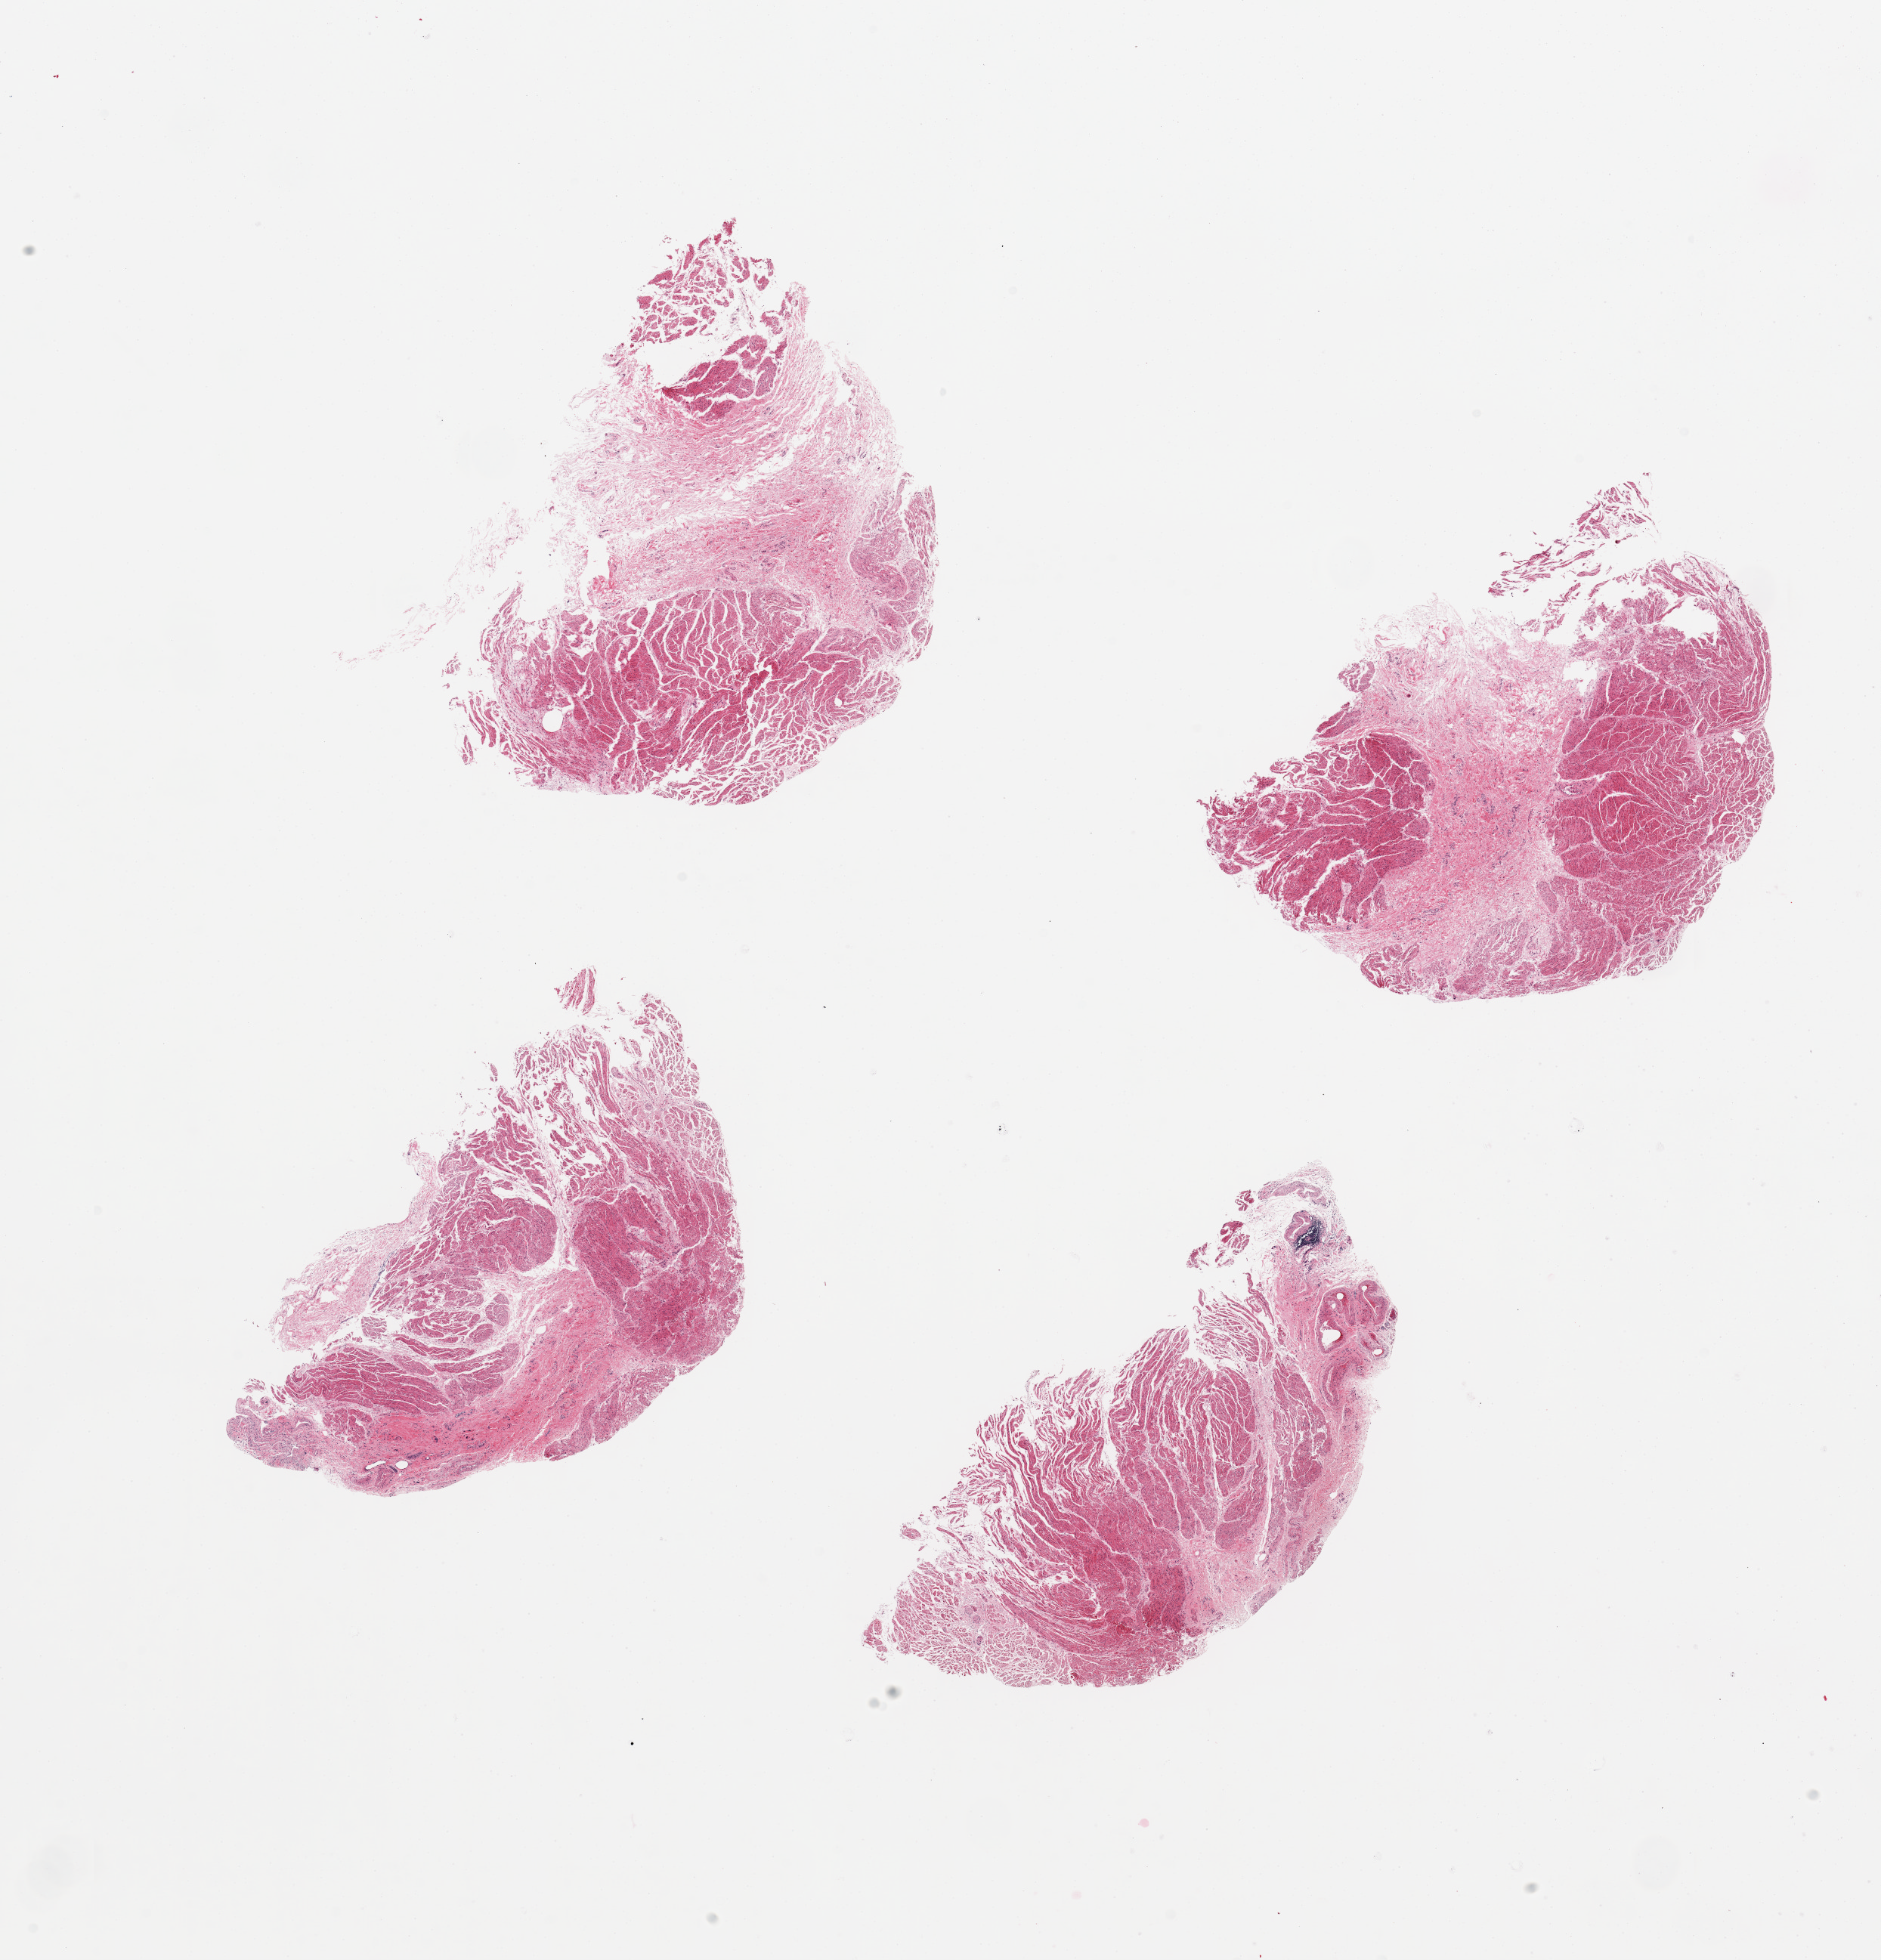
Whole-slide image, hematoxylin and eosin (H&E) stain, brightfield, whole scanned area (about 19.7 x 20.5 mm) shown as a low-resolution overview; PAXgene-fixed, paraffin-embedded tissue; target tissue: gastroesophageal junction; tissue donor sample. Male donor.
Review note (as recorded): 4 pieces.